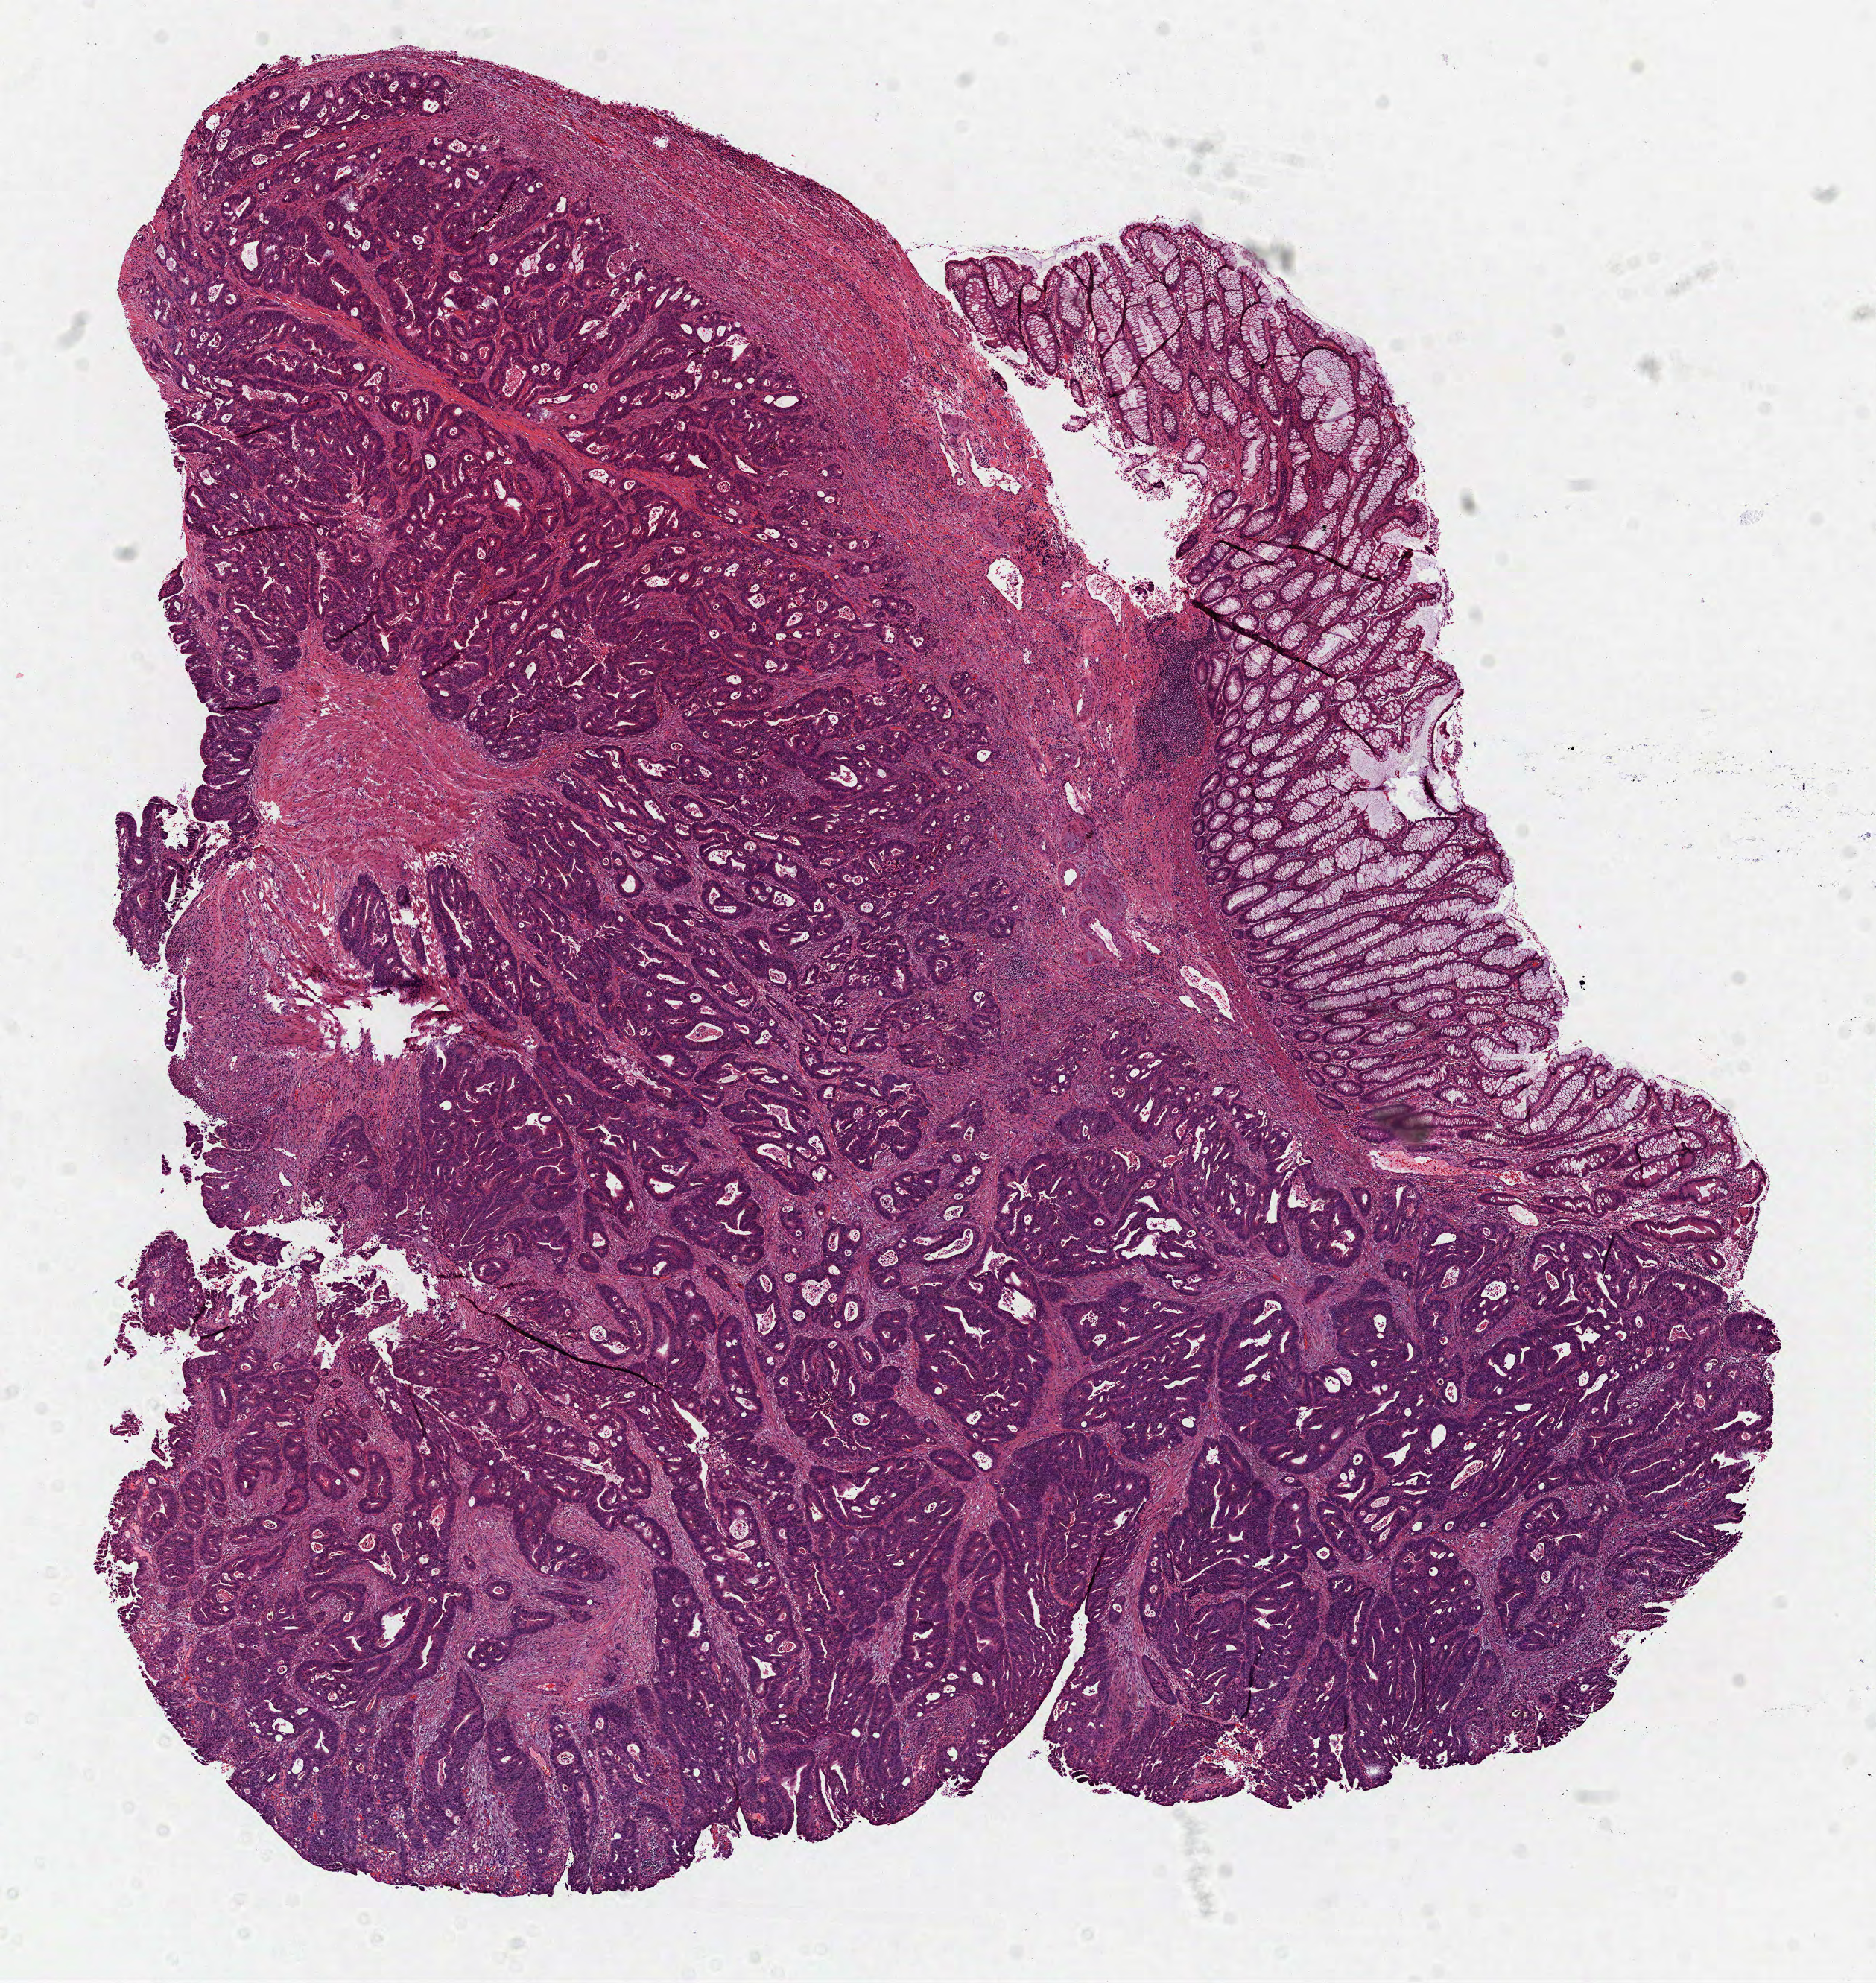
Whole-slide histology image, Hematoxylin and eosin (H&E) stained, low-resolution overview of the scanned area, about 10.2 x 10.7 mm (acquisition: 40x scan). Formalin-fixed paraffin-embedded (FFPE) diagnostic section. Primary tumour sample from the colon. Female patient; age at initial diagnosis 72 years.
- AJCC pathologic stage: II (6th edition)
- lymph nodes positive (case pathology): 0 of 34 examined
- histologic diagnosis: Adenocarcinoma, NOS (hepatic flexure of colon)